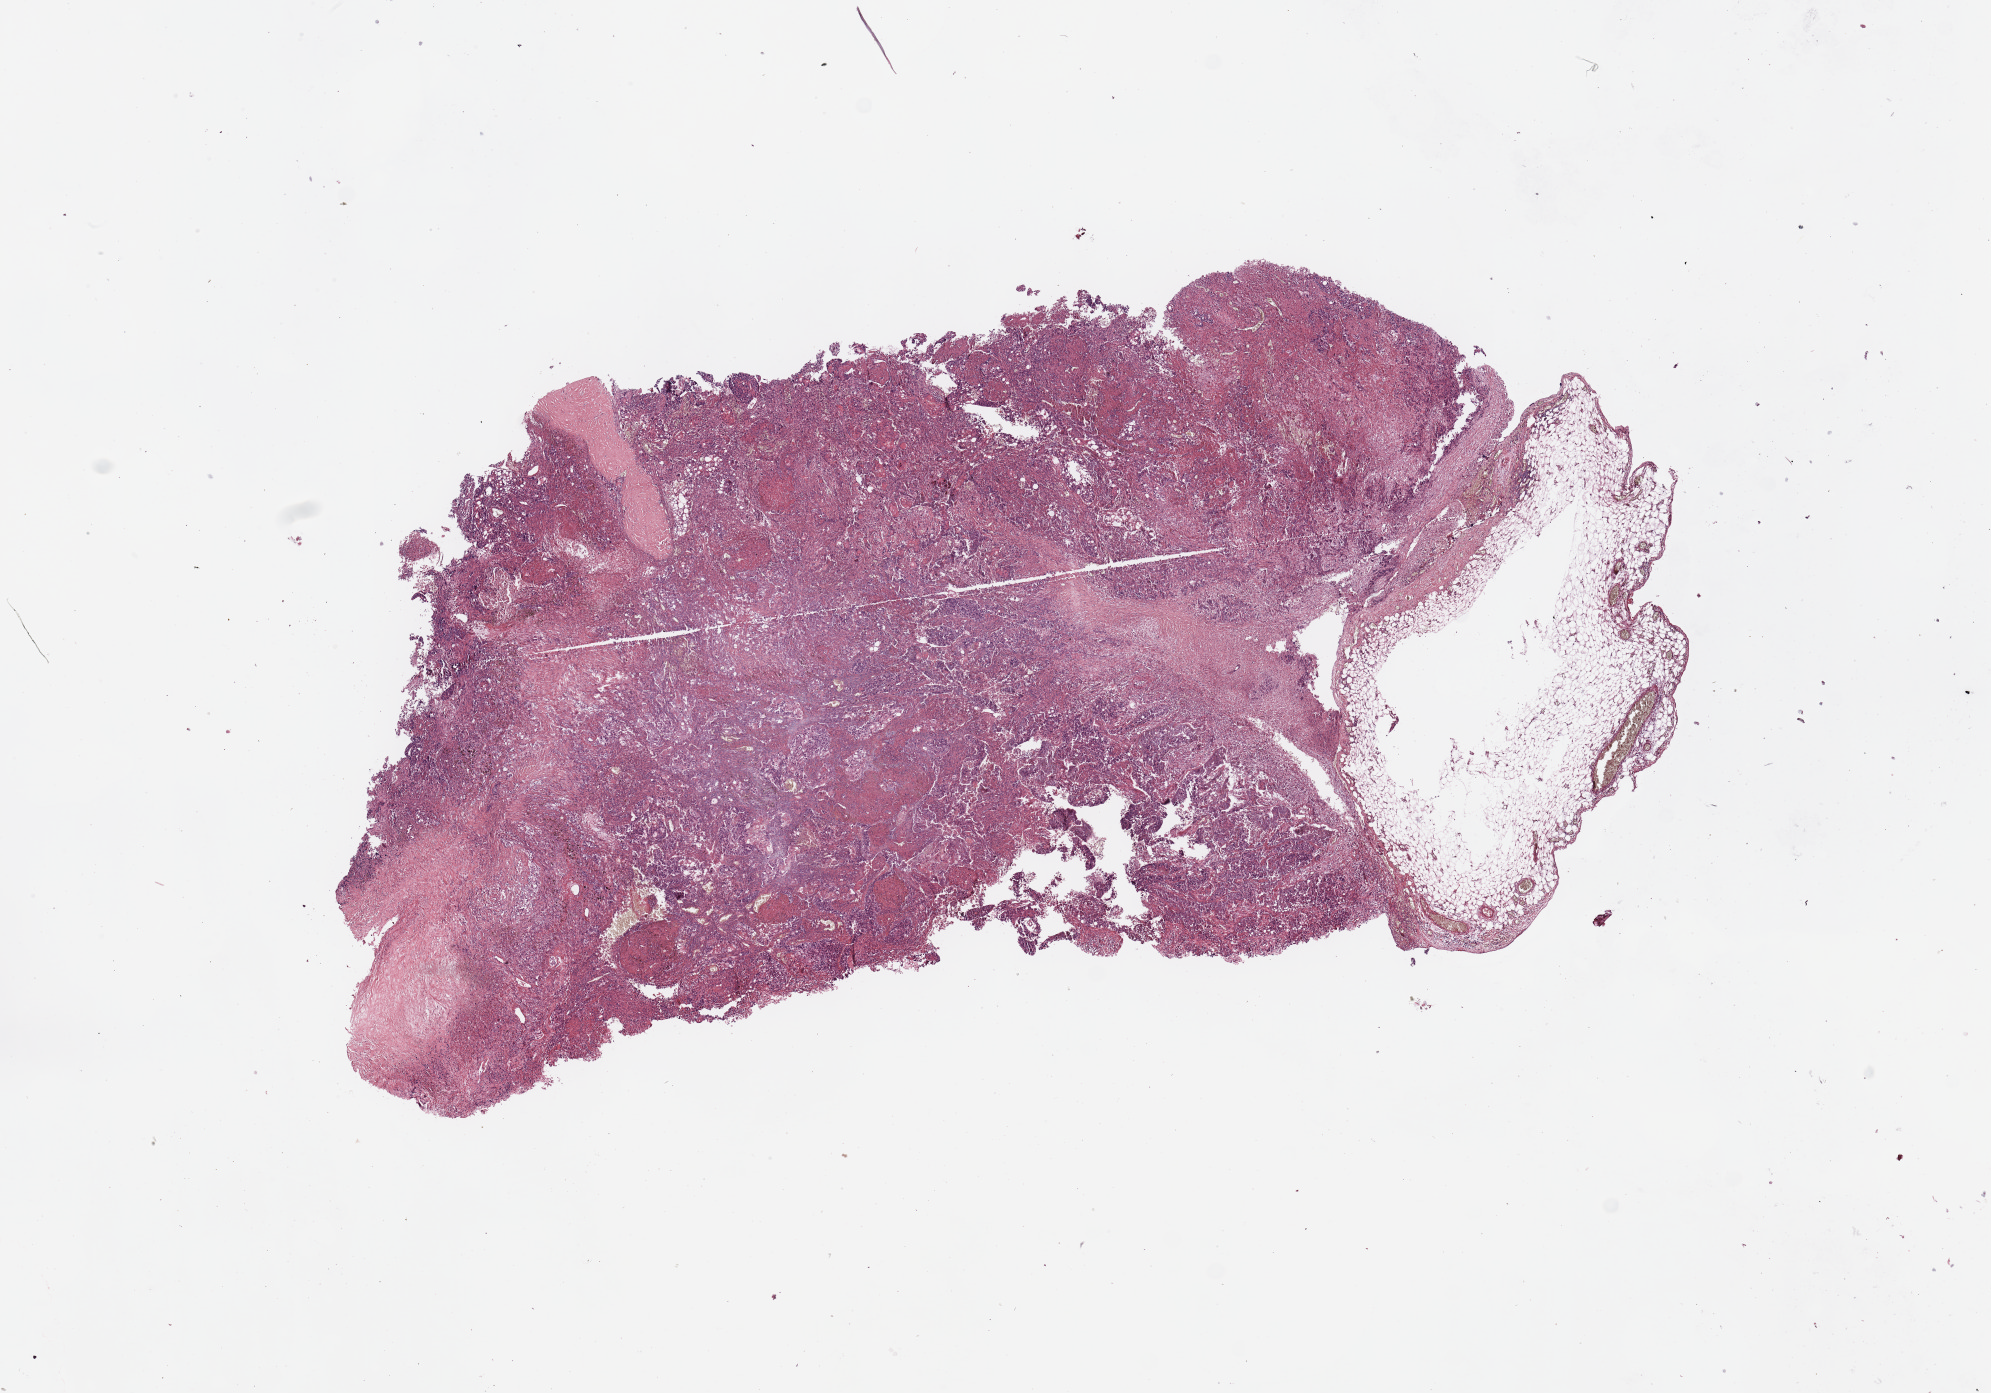
H&E whole-slide image — whole scanned area (about 15.8 x 11.0 mm, slide scanned at 20x) shown as a low-resolution overview, lung, tumour tissue. Patient: male, age 70 years. Histologic grade: G2 (moderately differentiated).
AJCC pathologic stage: IB. Primary tumour site (as recorded): right middle lobe. Diagnosis: Squamous cell carcinoma, NOS.